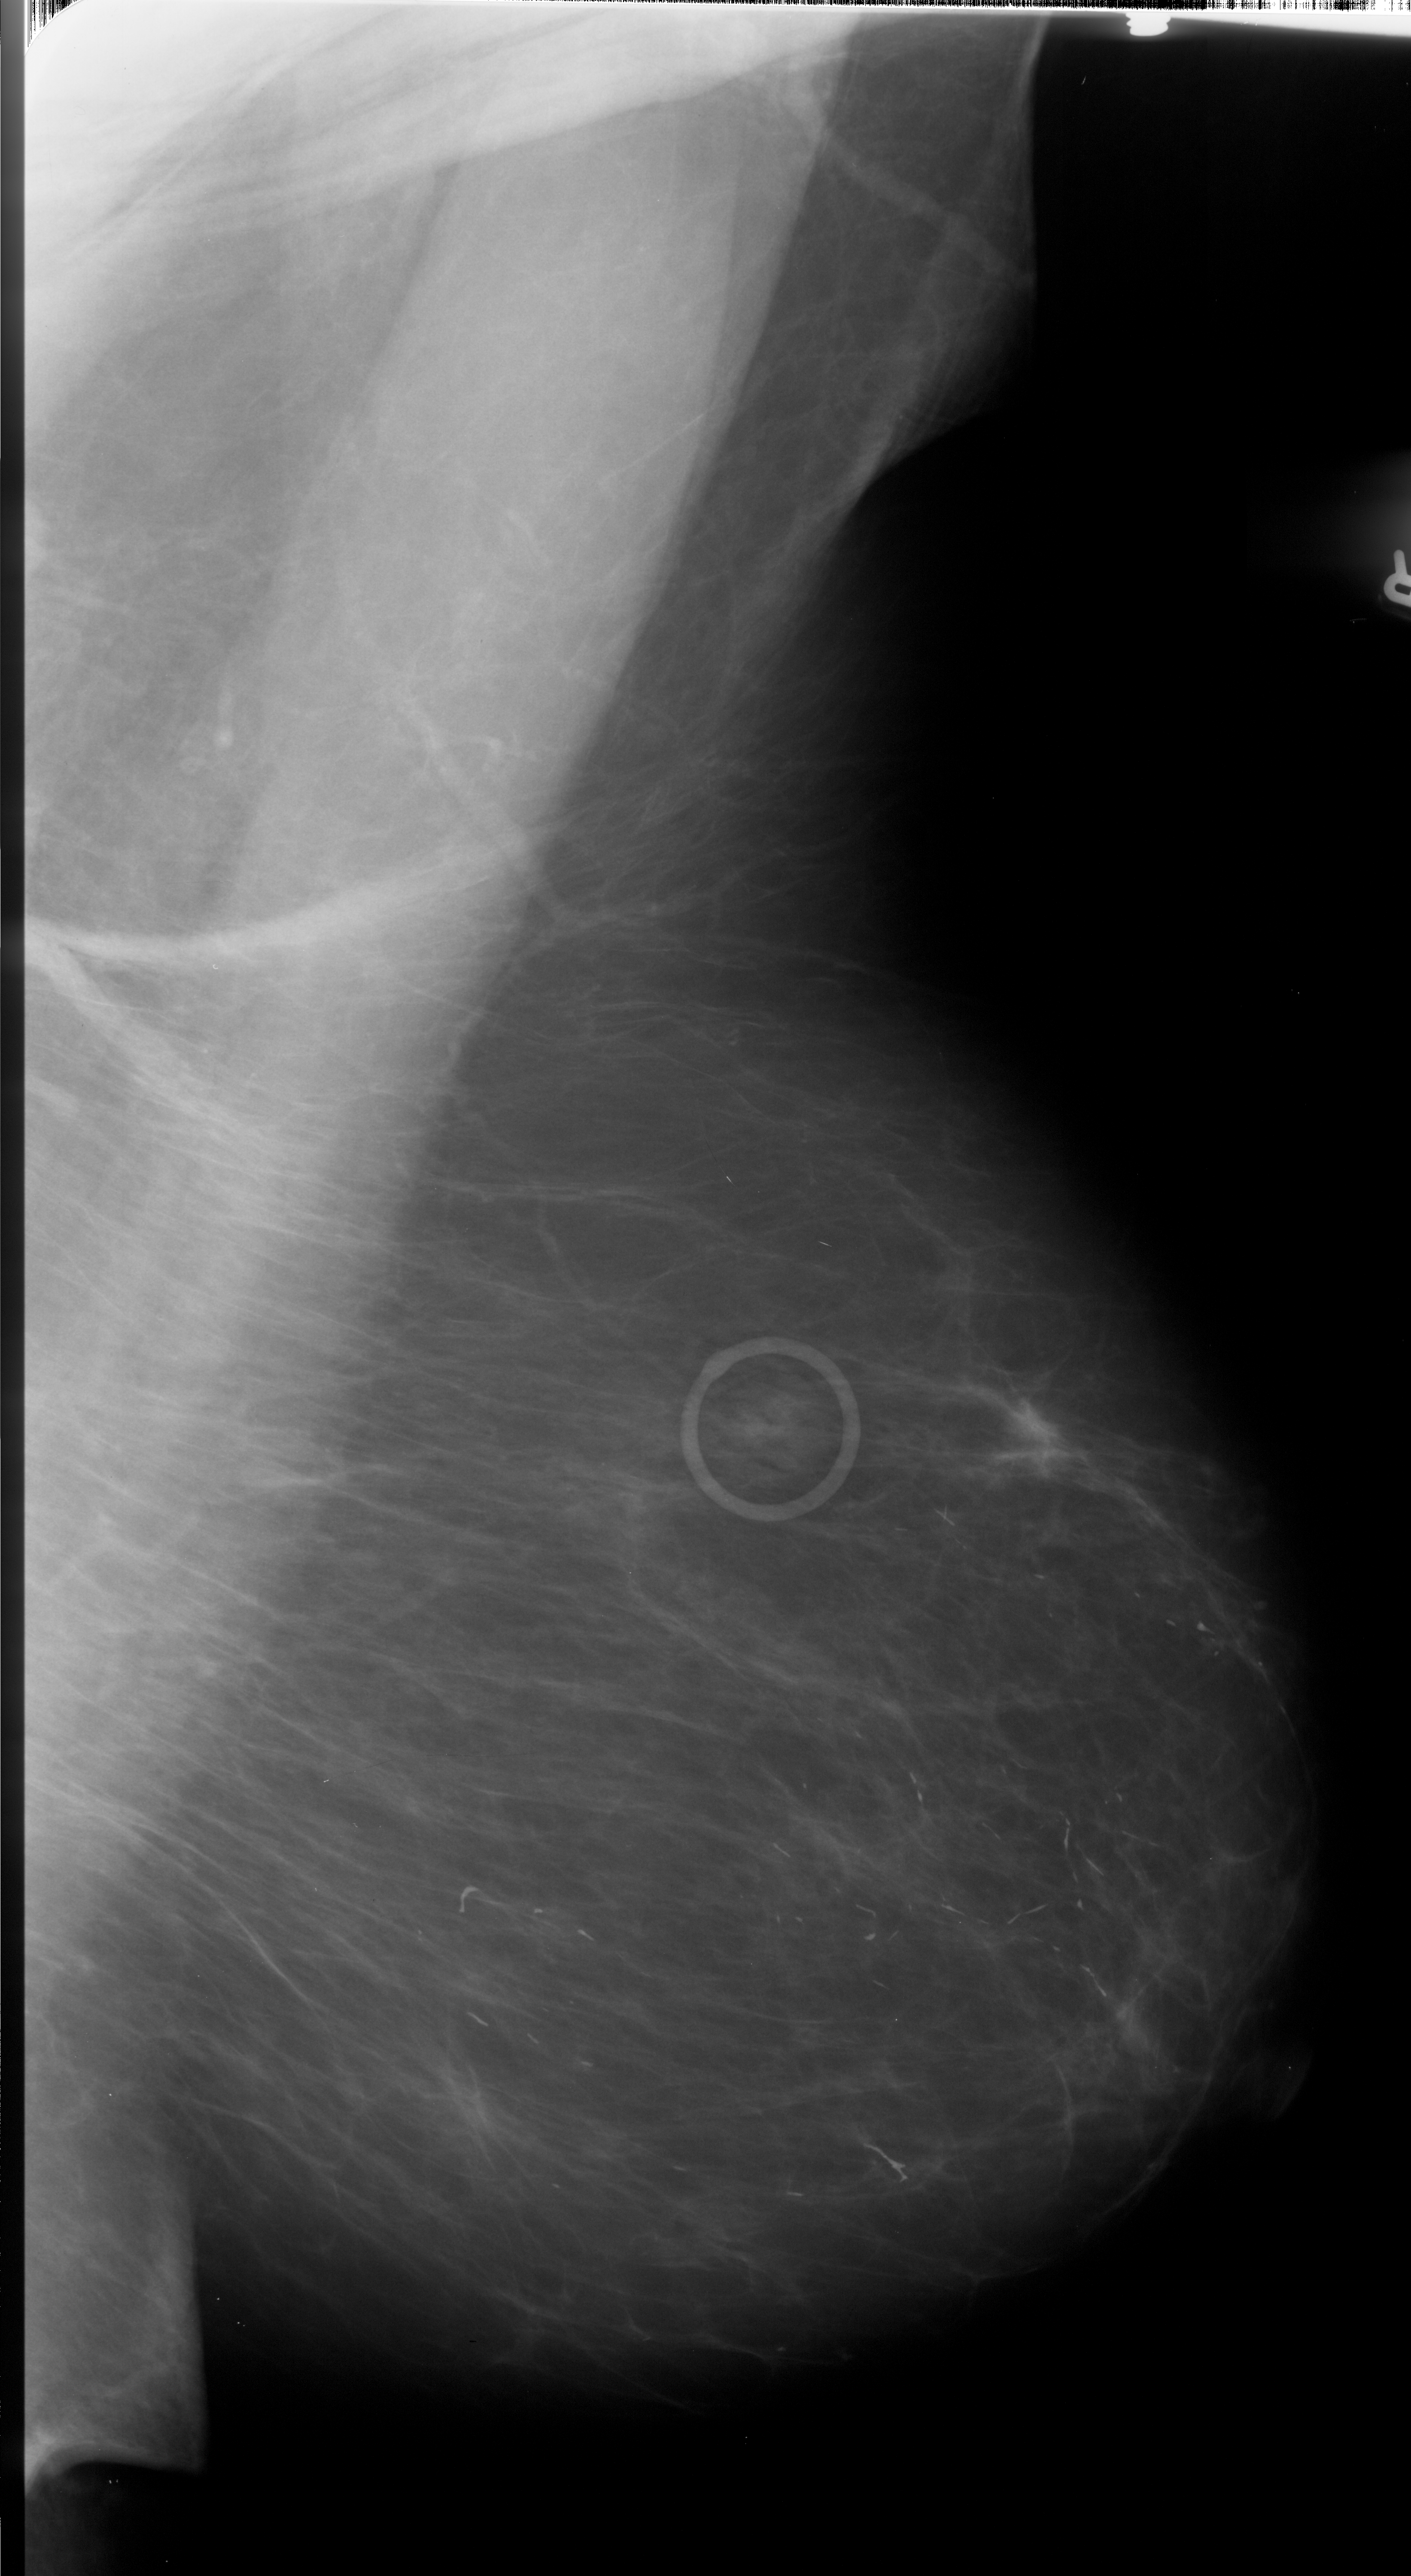
Scanned film-screen mammogram, right breast, mediolateral oblique (MLO) view, breast composition: almost entirely fatty (BI-RADS density category 1 of 4).
Marked findings (only marked abnormalities are described; nothing is implied about the rest of the image): mass, shape irregular, margins spiculated; BI-RADS assessment category 5; subtlety rating 4 on a 1 (subtle) to 5 (obvious) scale; pathology (as recorded): malignant.